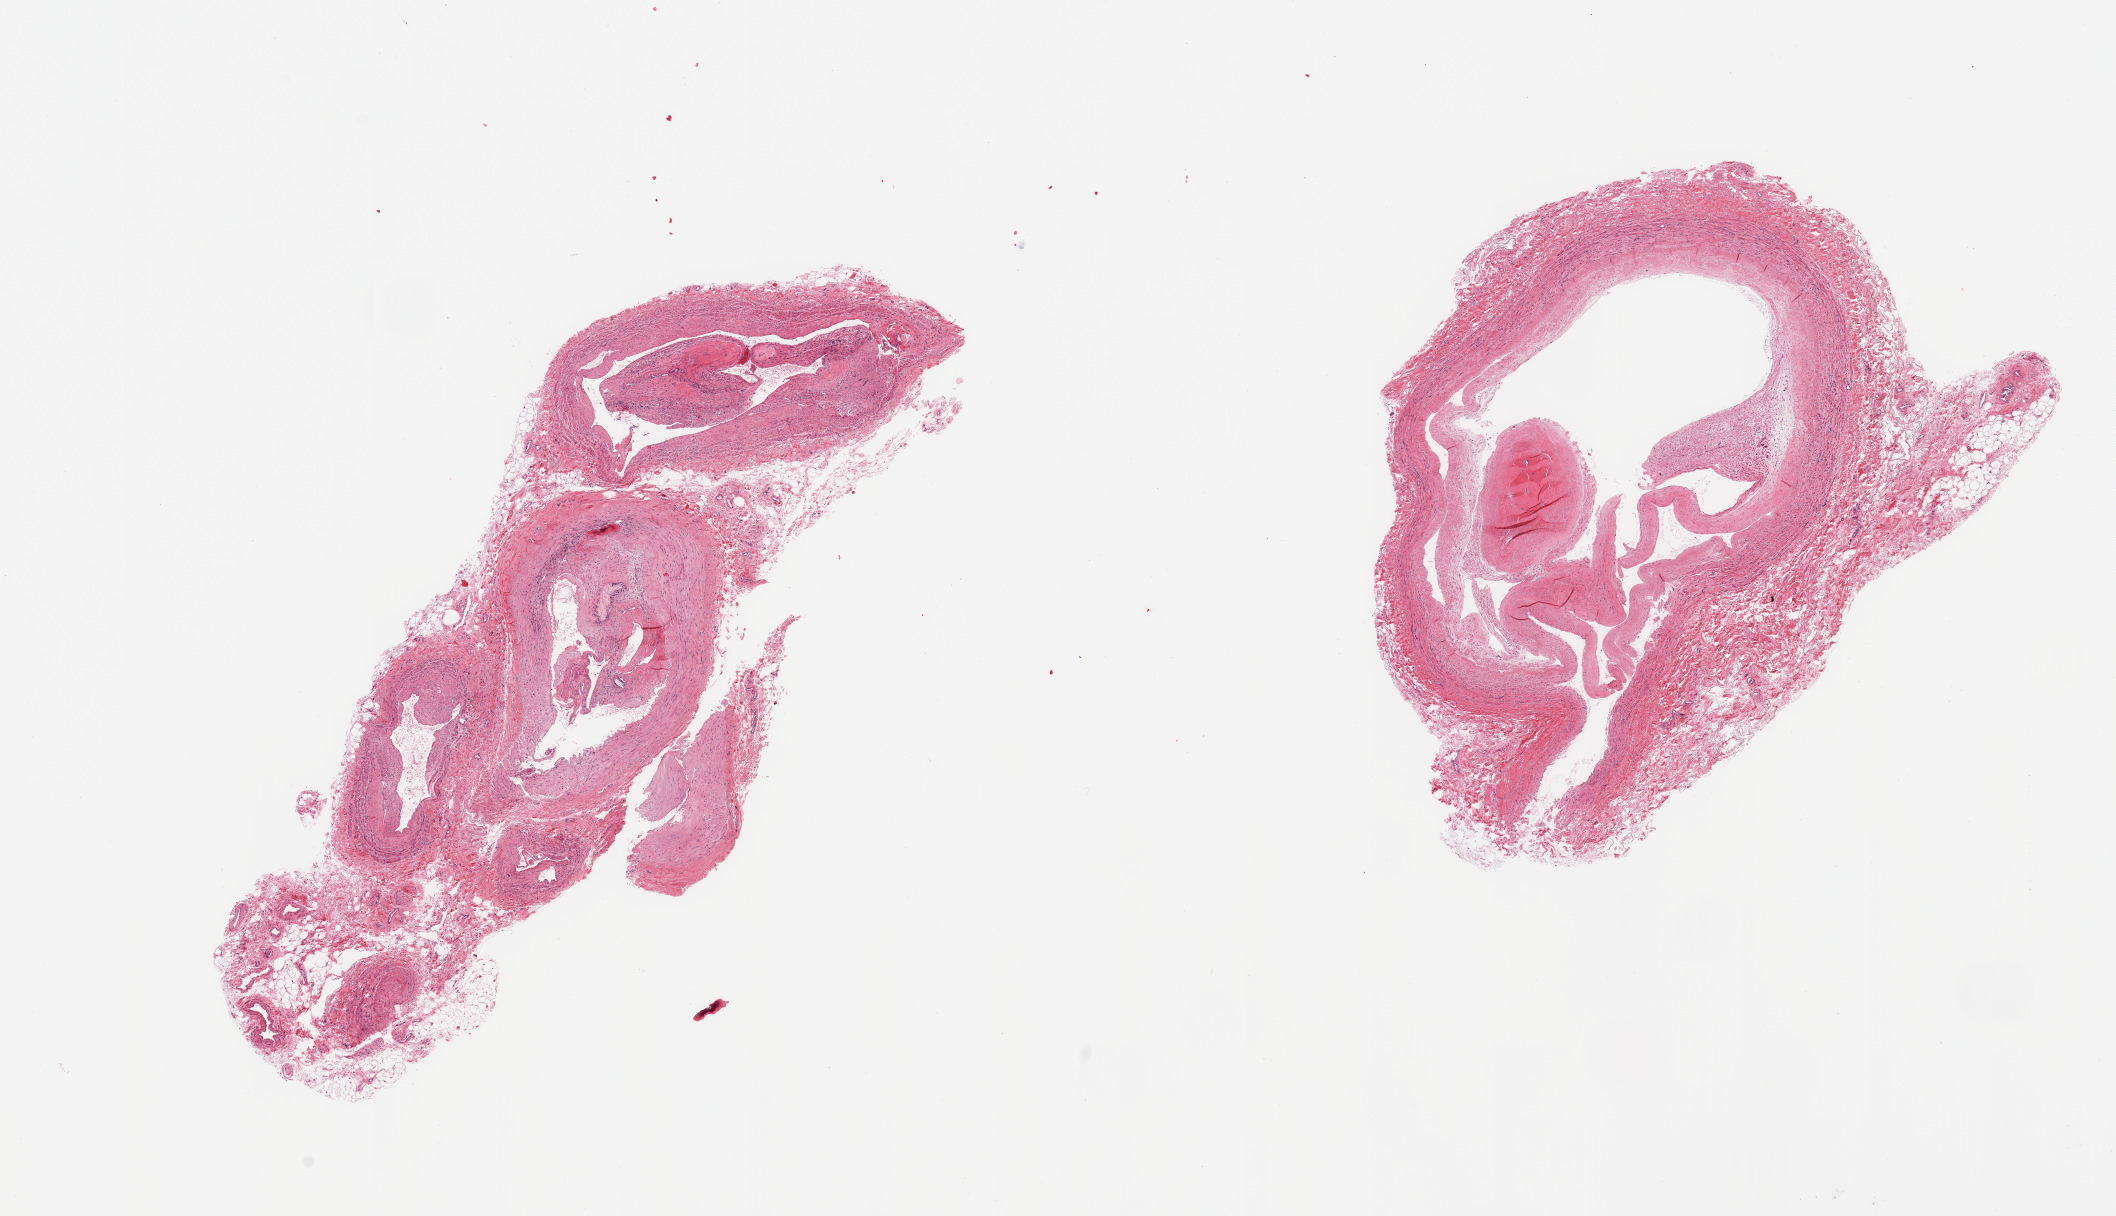
Haematoxylin and eosin whole-slide image — whole scanned area (about 16.7 x 9.6 mm, acquisition: 20x scan) shown as a low-resolution overview. PAXgene-fixed, paraffin-embedded tissue. Section of tibial artery (target tissue). Donor tissue sample. Donor: female.
Pathologist's review note for this sample: 2 pieces: 1 sample contains arteries with organized thrombi; other is a vein with organized thrombi.